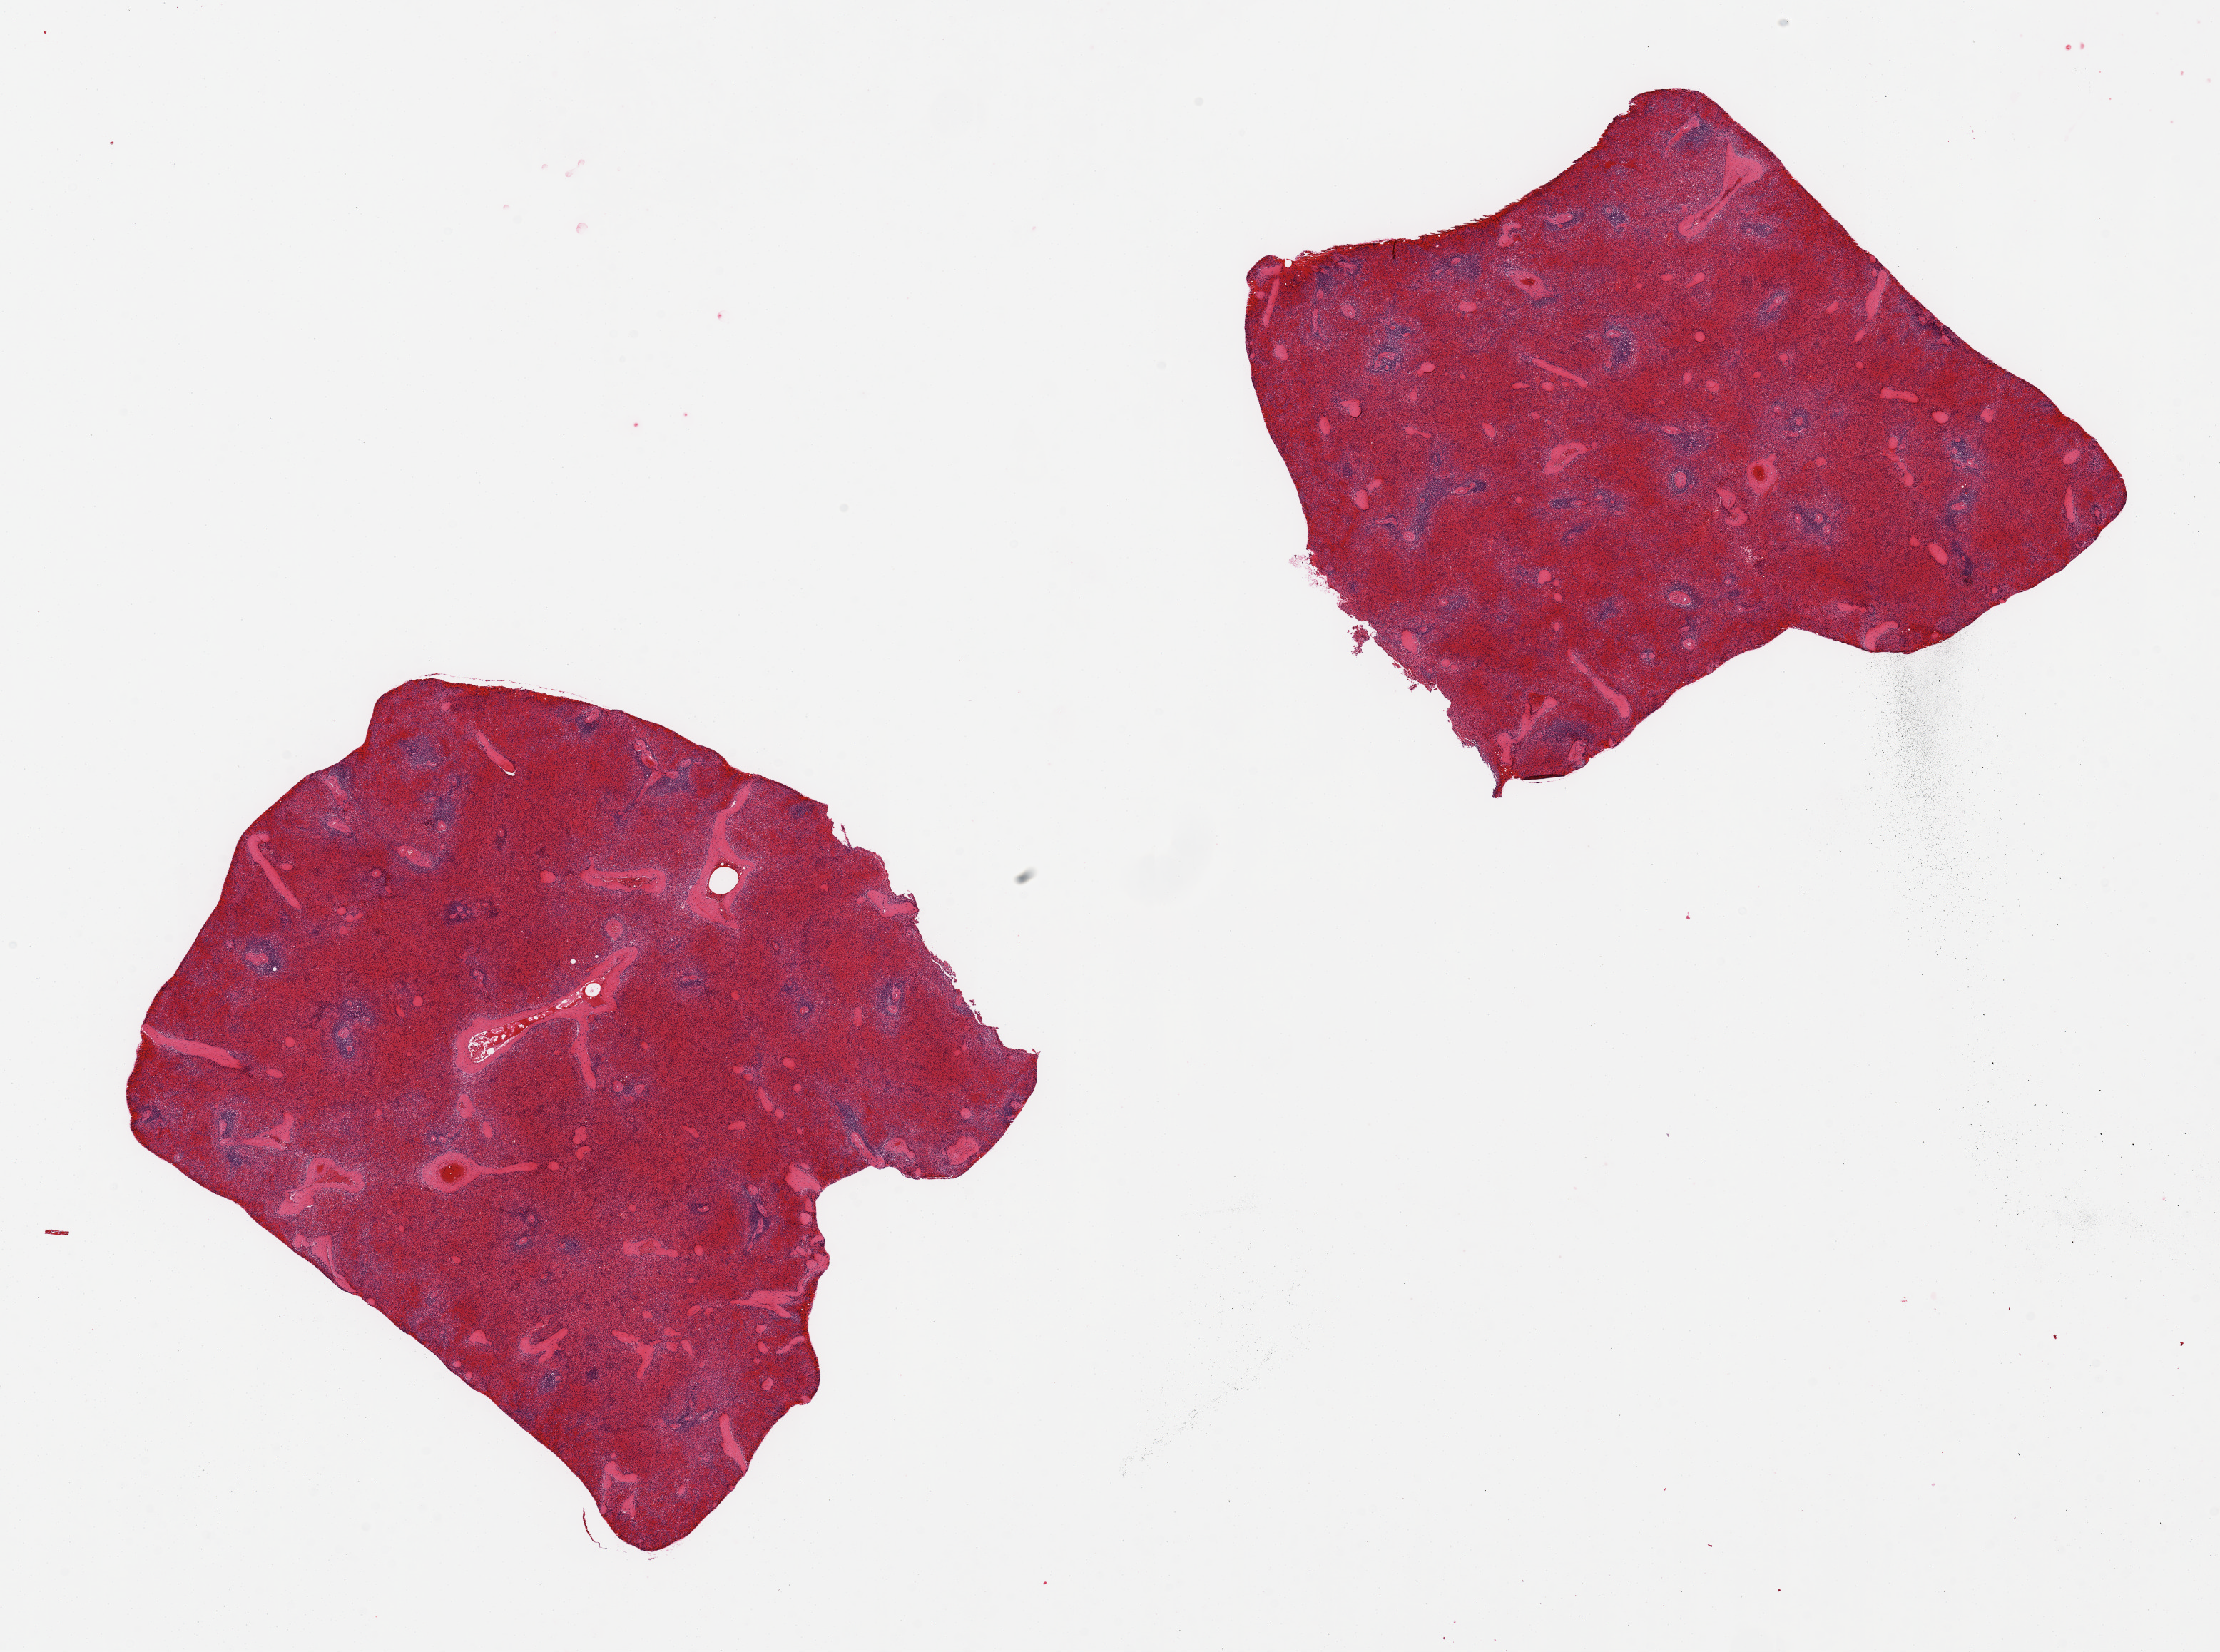
Digitized hematoxylin and eosin (H&E)-stained section, shown as a low-resolution overview of the whole scanned area (about 24.6 x 18.3 mm, from a 20x scan), PAXgene-fixed, paraffin-embedded tissue, target tissue: spleen, donor tissue sample. Donor sex: female.
Reviewer comment on this tissue sample: 2 pieces, congested.